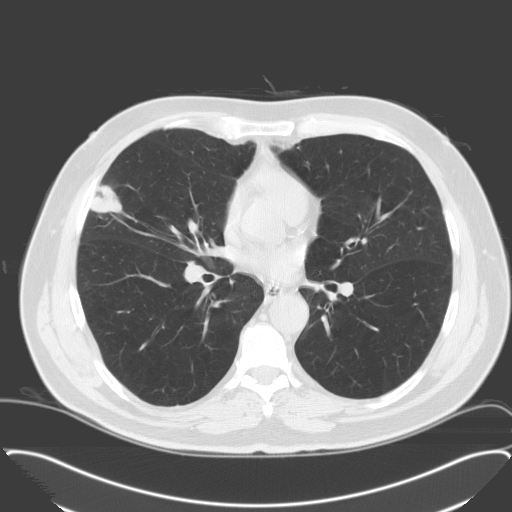
Low-dose screening chest CT, axial slice, third screening round (two years after baseline), lung window (W 1500 / L -600 HU), 120 kVp, 512 × 512 image matrix. Male, age 65 years at enrolment.
• Expert reader's lesion annotation, bounding box [x1, y1, x2, y2] px = [73, 182, 129, 235].
• The exam's reader record, not a measurement of the box and not confirmed to be the same lesion: non-calcified nodule or mass ≥4 mm, right middle lobe, 28 × 23 mm, spiculated (stellate) margins, soft tissue attenuation, pre-existing on the prior screen: no.
• Official screen result: positive, other.